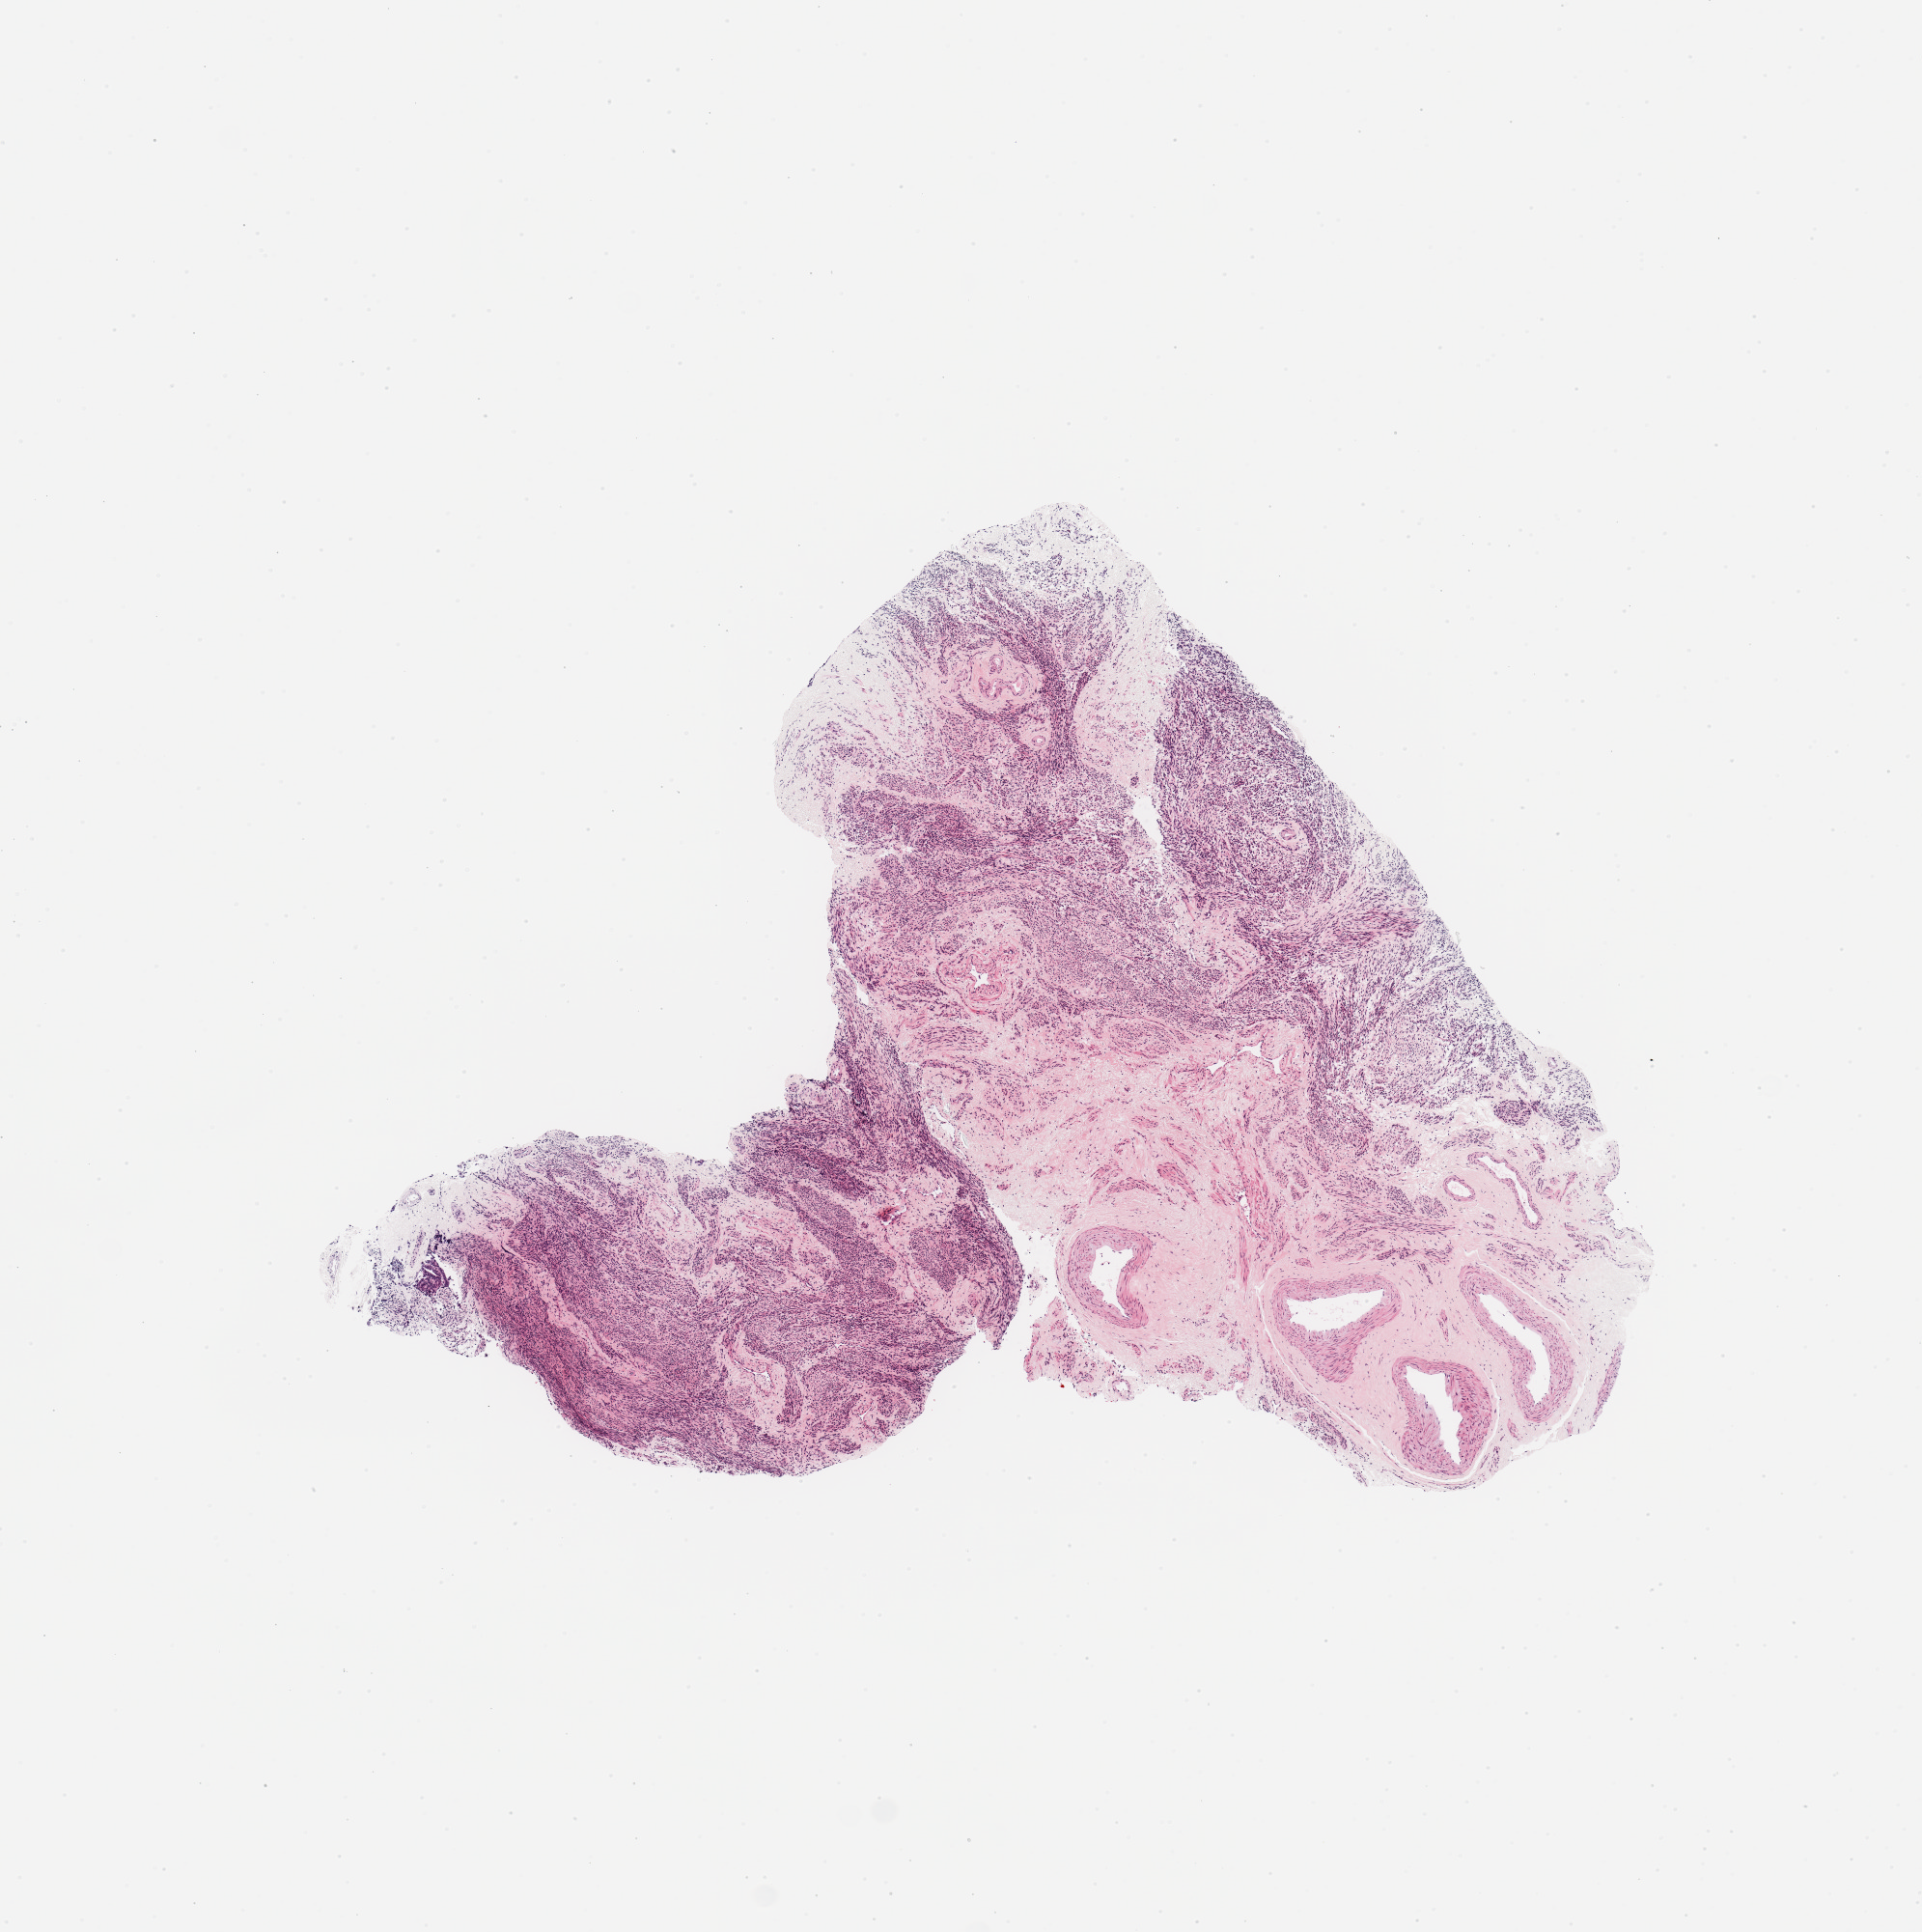
H&E-stained whole-slide image — low-resolution overview of the scanned area, about 7.9 x 7.9 mm (slide scanned at 20x), normal (non-tumour) tissue sample, uterus. Patient: female, age 62 years.
This section: normal (non-tumour) tissue from the same patient. Patient diagnosis: Endometrioid adenocarcinoma, NOS.